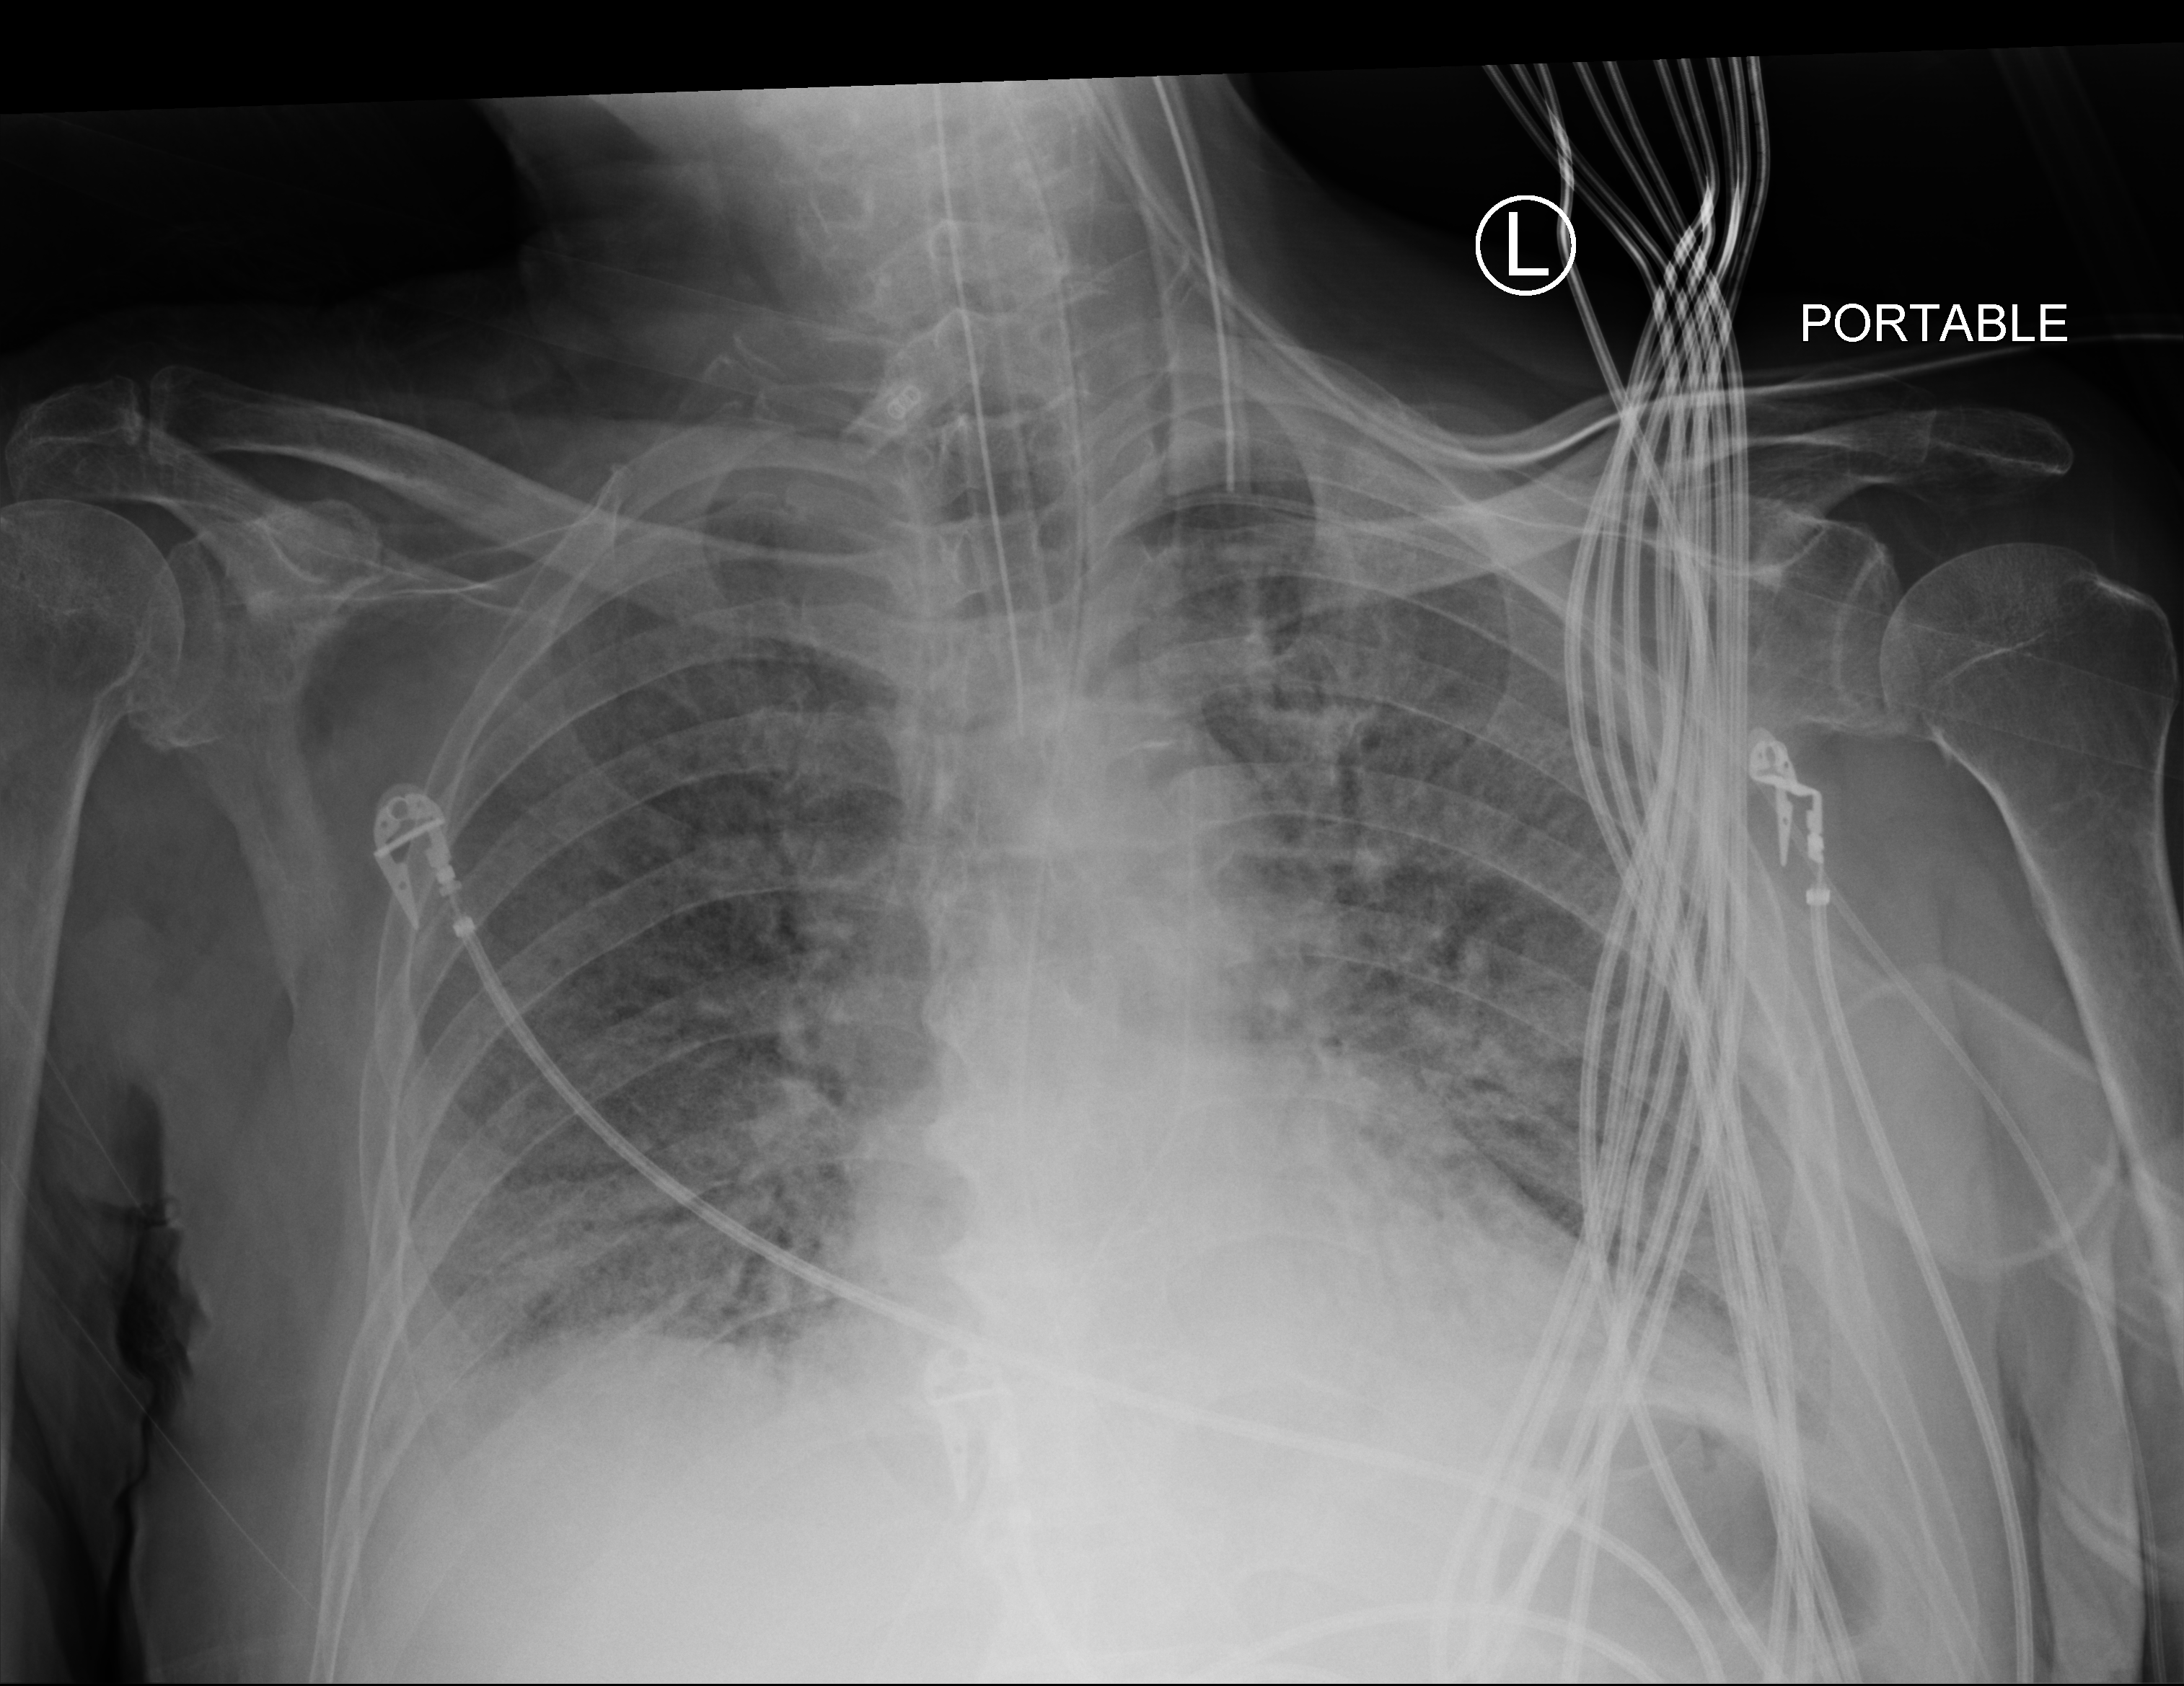
Bedside chest radiograph (computed radiography); anteroposterior (AP) projection. Male patient hospitalised with COVID-19, age 75–90 years.
Admission-level facts for this patient (not findings on this image; timing relative to this image not recorded): mechanically ventilated during this hospital stay: yes; other chronic lung disease (admission record): no.